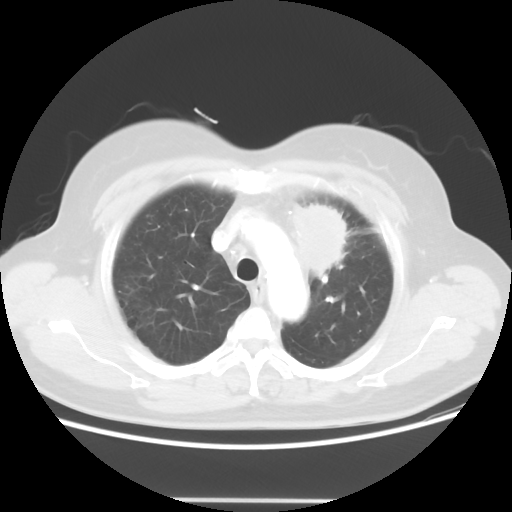
Chest CT, one axial slice; position 42 of 52 along the scan axis; lung window (W 1500 / L -600 HU); 512 × 512 image matrix, field of view 382 × 382 mm. Patient: female, 52 years. From the clinical record (not read from this slice): clinical TNM (as recorded): T2 N3 M0.
Annotated regions visible in this slice (rectangle marked by the reading radiologist):
- lung tumour (recorded histology: adenocarcinoma): bounding box [x1, y1, x2, y2] px = [287, 197, 351, 276]